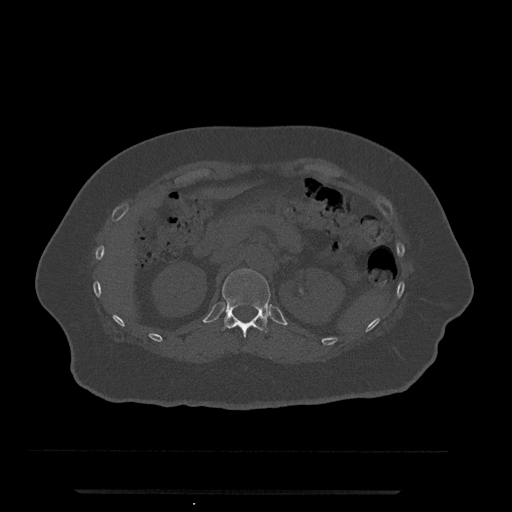
CT including the spine, one axial slice; position 167 of 797 along the scan axis; reconstruction kernel Br40s/3; bone window (W 1800 / L 400 HU); 512 × 512 image matrix, field of view 440 × 440 mm. Patient: female, 51 years. Case-level facts recorded for this patient, not image findings: primary cancer: neuro; vertebrae with lytic lesions (as recorded): T8.
Structures marked on this image (semi-automatic segmentation, software-assisted and operator-edited):
- T12 vertebra: box from (x=222, y=269) to (x=270, y=337) px